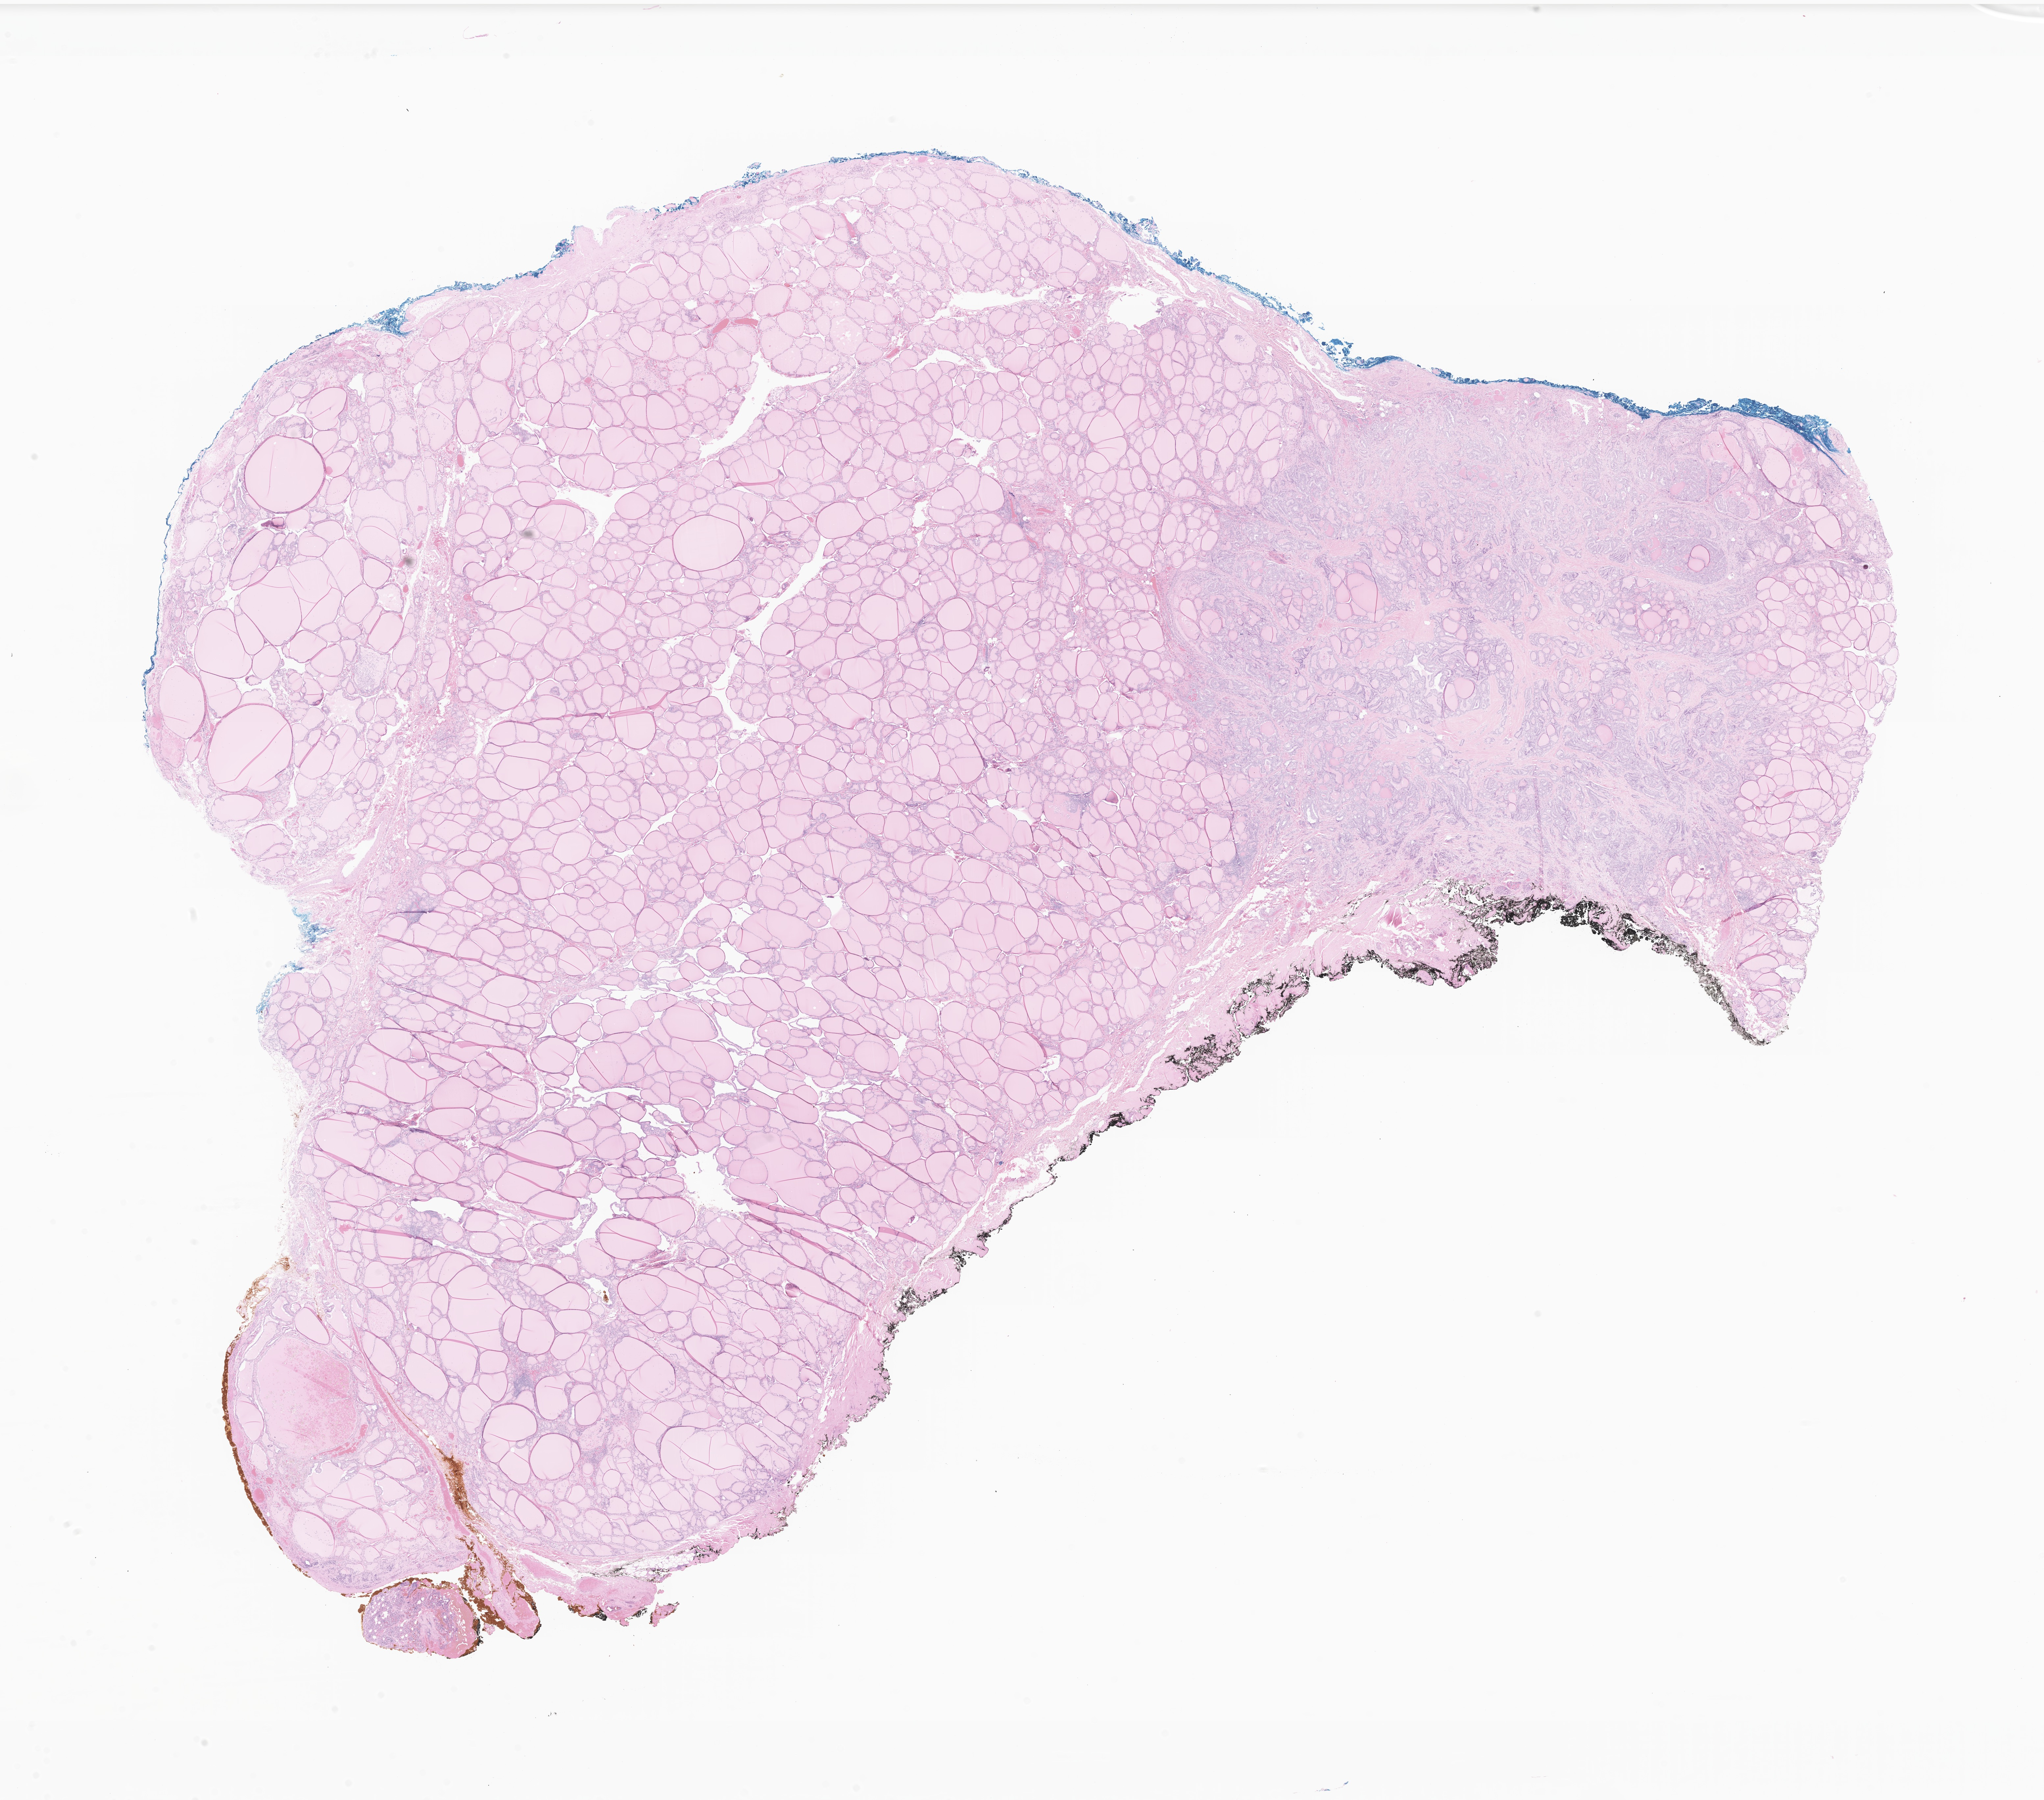
Hematoxylin and eosin (H&E) whole-slide image of tumor tissue from the thyroid, shown as a low-resolution overview of the whole scanned area (about 26.2 x 23.1 mm); FFPE section. Patient female; age 210 months (17 years 6 months).
Diagnosis (ICD-O-3 morphology term): Carcinoma, NOS.